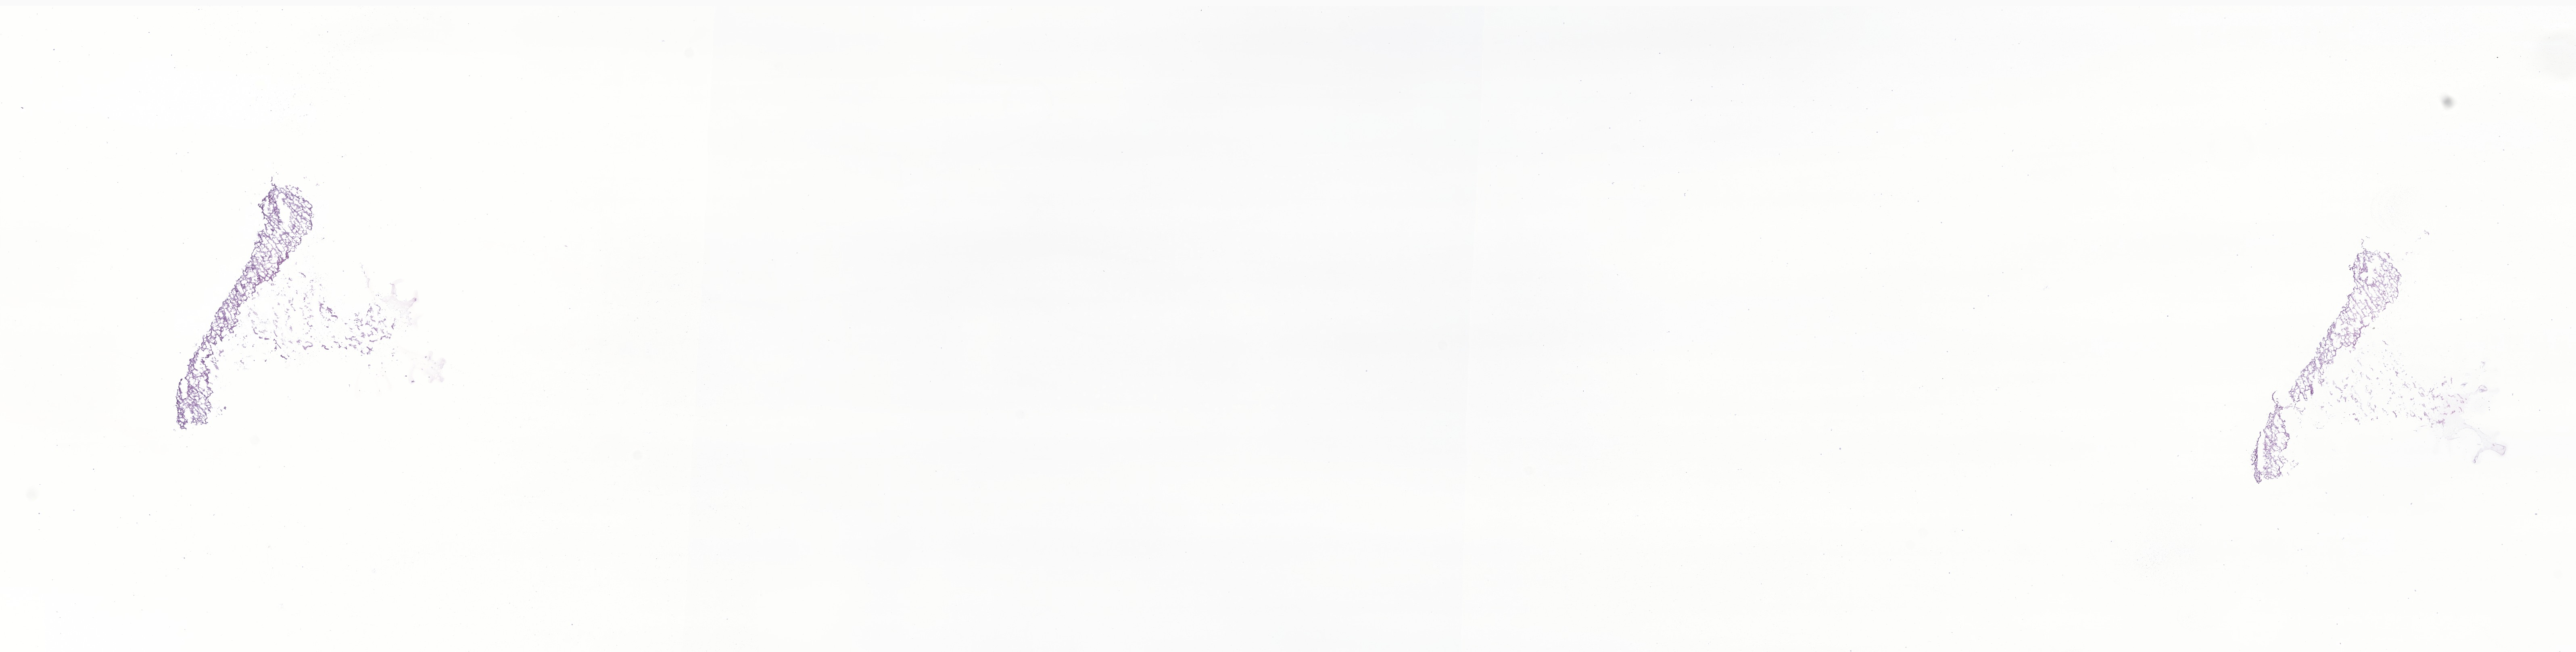
Hematoxylin and eosin (H&E) whole-slide image of tumor tissue from the cerebellum — whole scanned area (about 26.9 x 6.8 mm) shown as a low-resolution overview; frozen section. Patient: male, age 59 months (4 years 11 months).
Diagnosis: Neoplasm, uncertain whether benign or malignant.